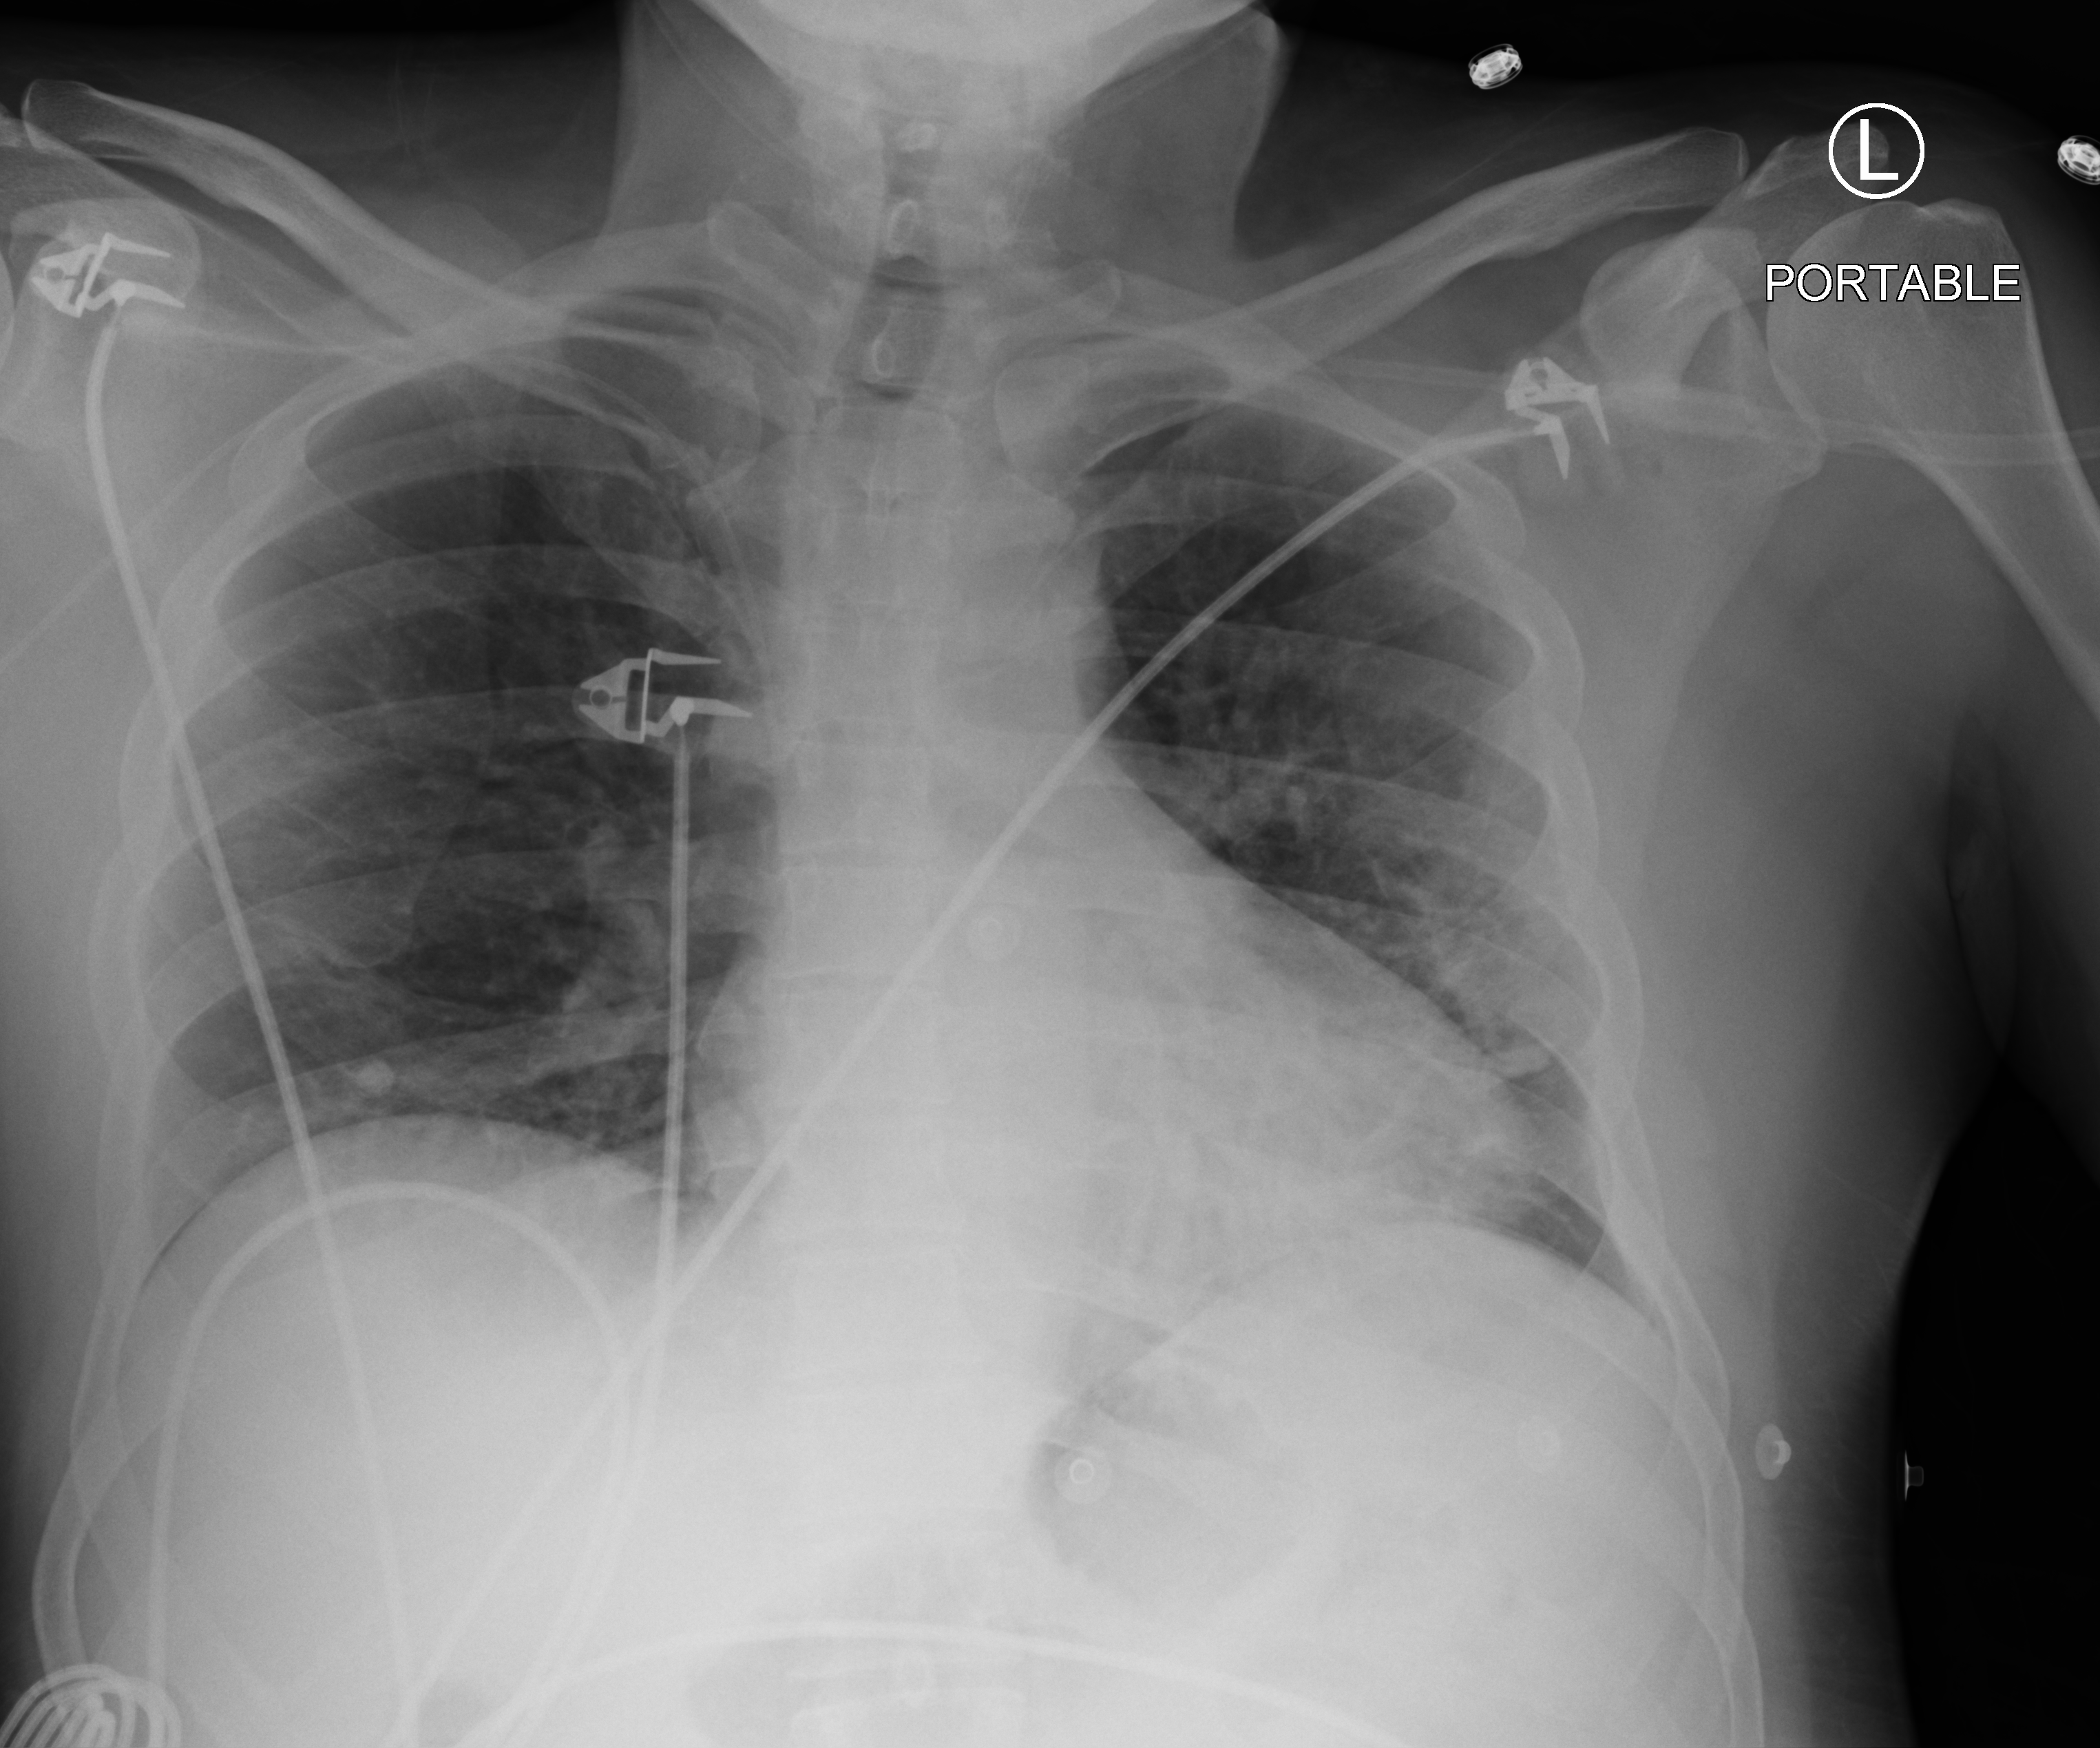
Bedside chest radiograph (computed radiography); anteroposterior (AP) projection. Patient hospitalised with COVID-19; male, aged 18–59 years.
Hospital-stay facts (about this admission, not read from this image; timing relative to this image not recorded):
- COPD (admission record): no
- admitted to intensive care during this hospital stay: no
- diabetes (admission record): no